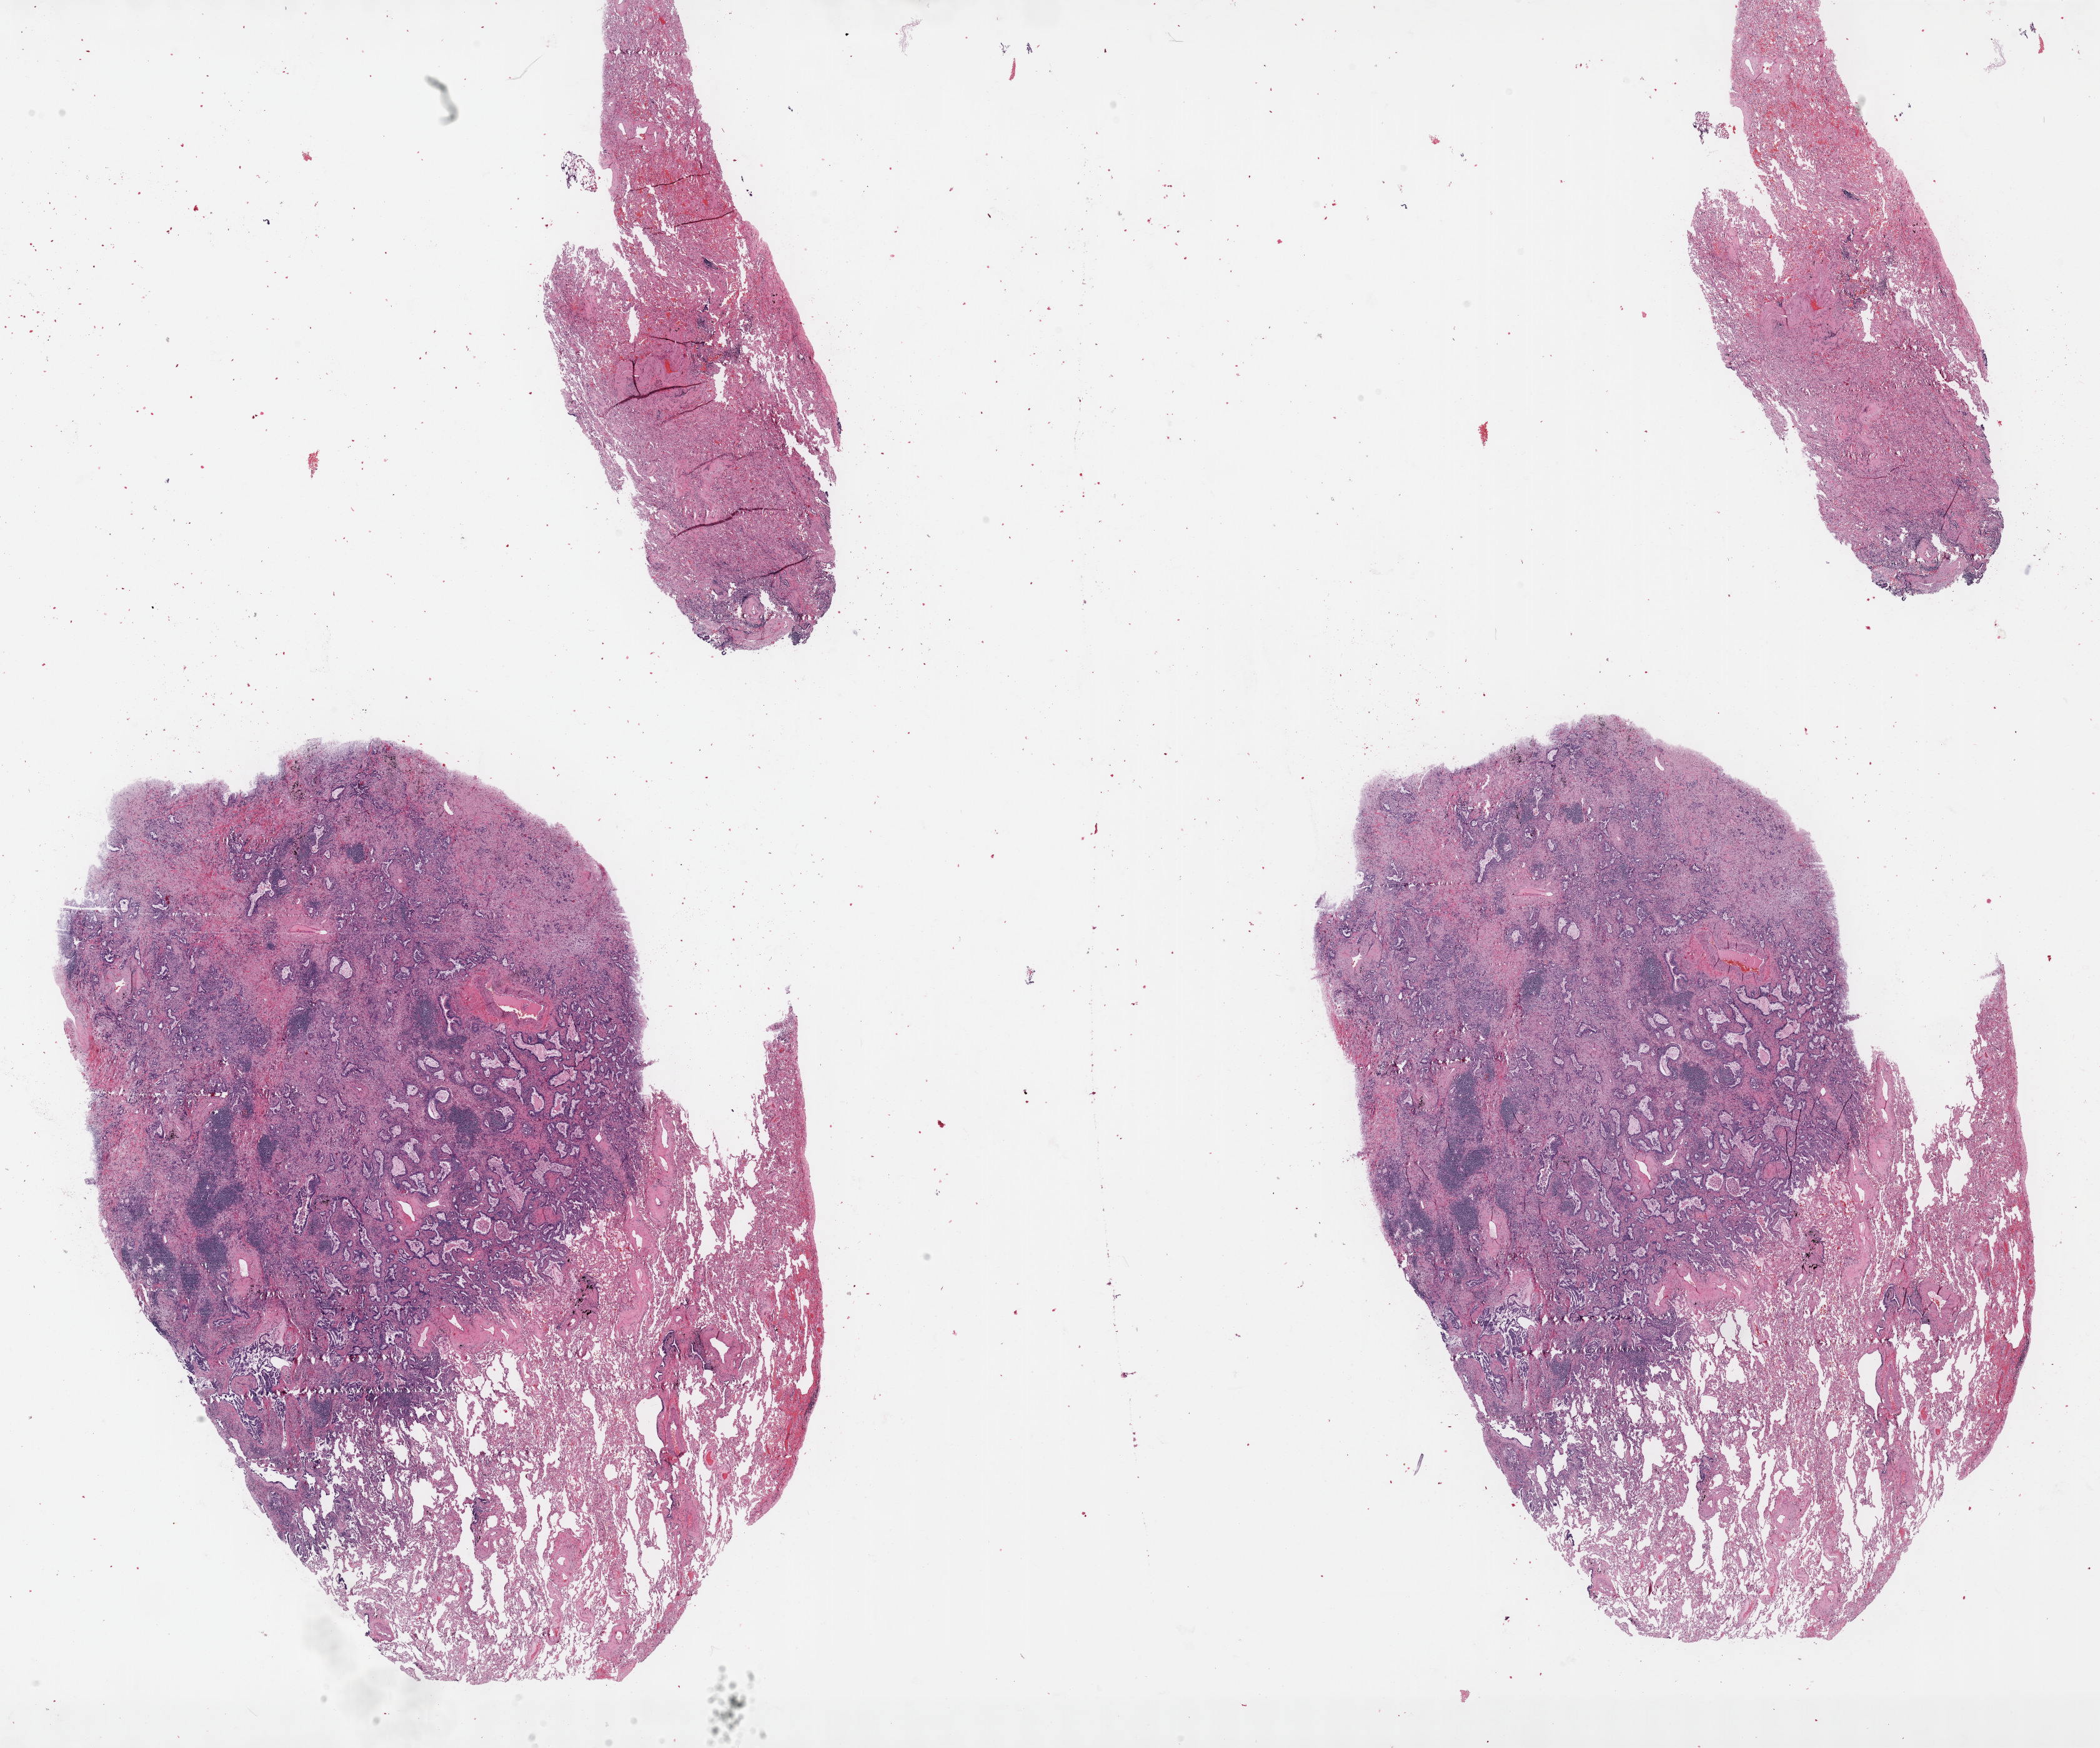
Whole-slide histology image, H&E-stained, shown as a low-resolution overview of the whole scanned area (about 27.2 x 22.6 mm). Formalin-fixed paraffin-embedded (FFPE) diagnostic section. Lung, primary tumour sample. Female patient; age at initial diagnosis 76 years.
AJCC pathologic stage: IB (6th edition). Laterality: right. TNM: T2 N0 M0. Diagnosis: Acinar cell carcinoma (lower lobe, lung).